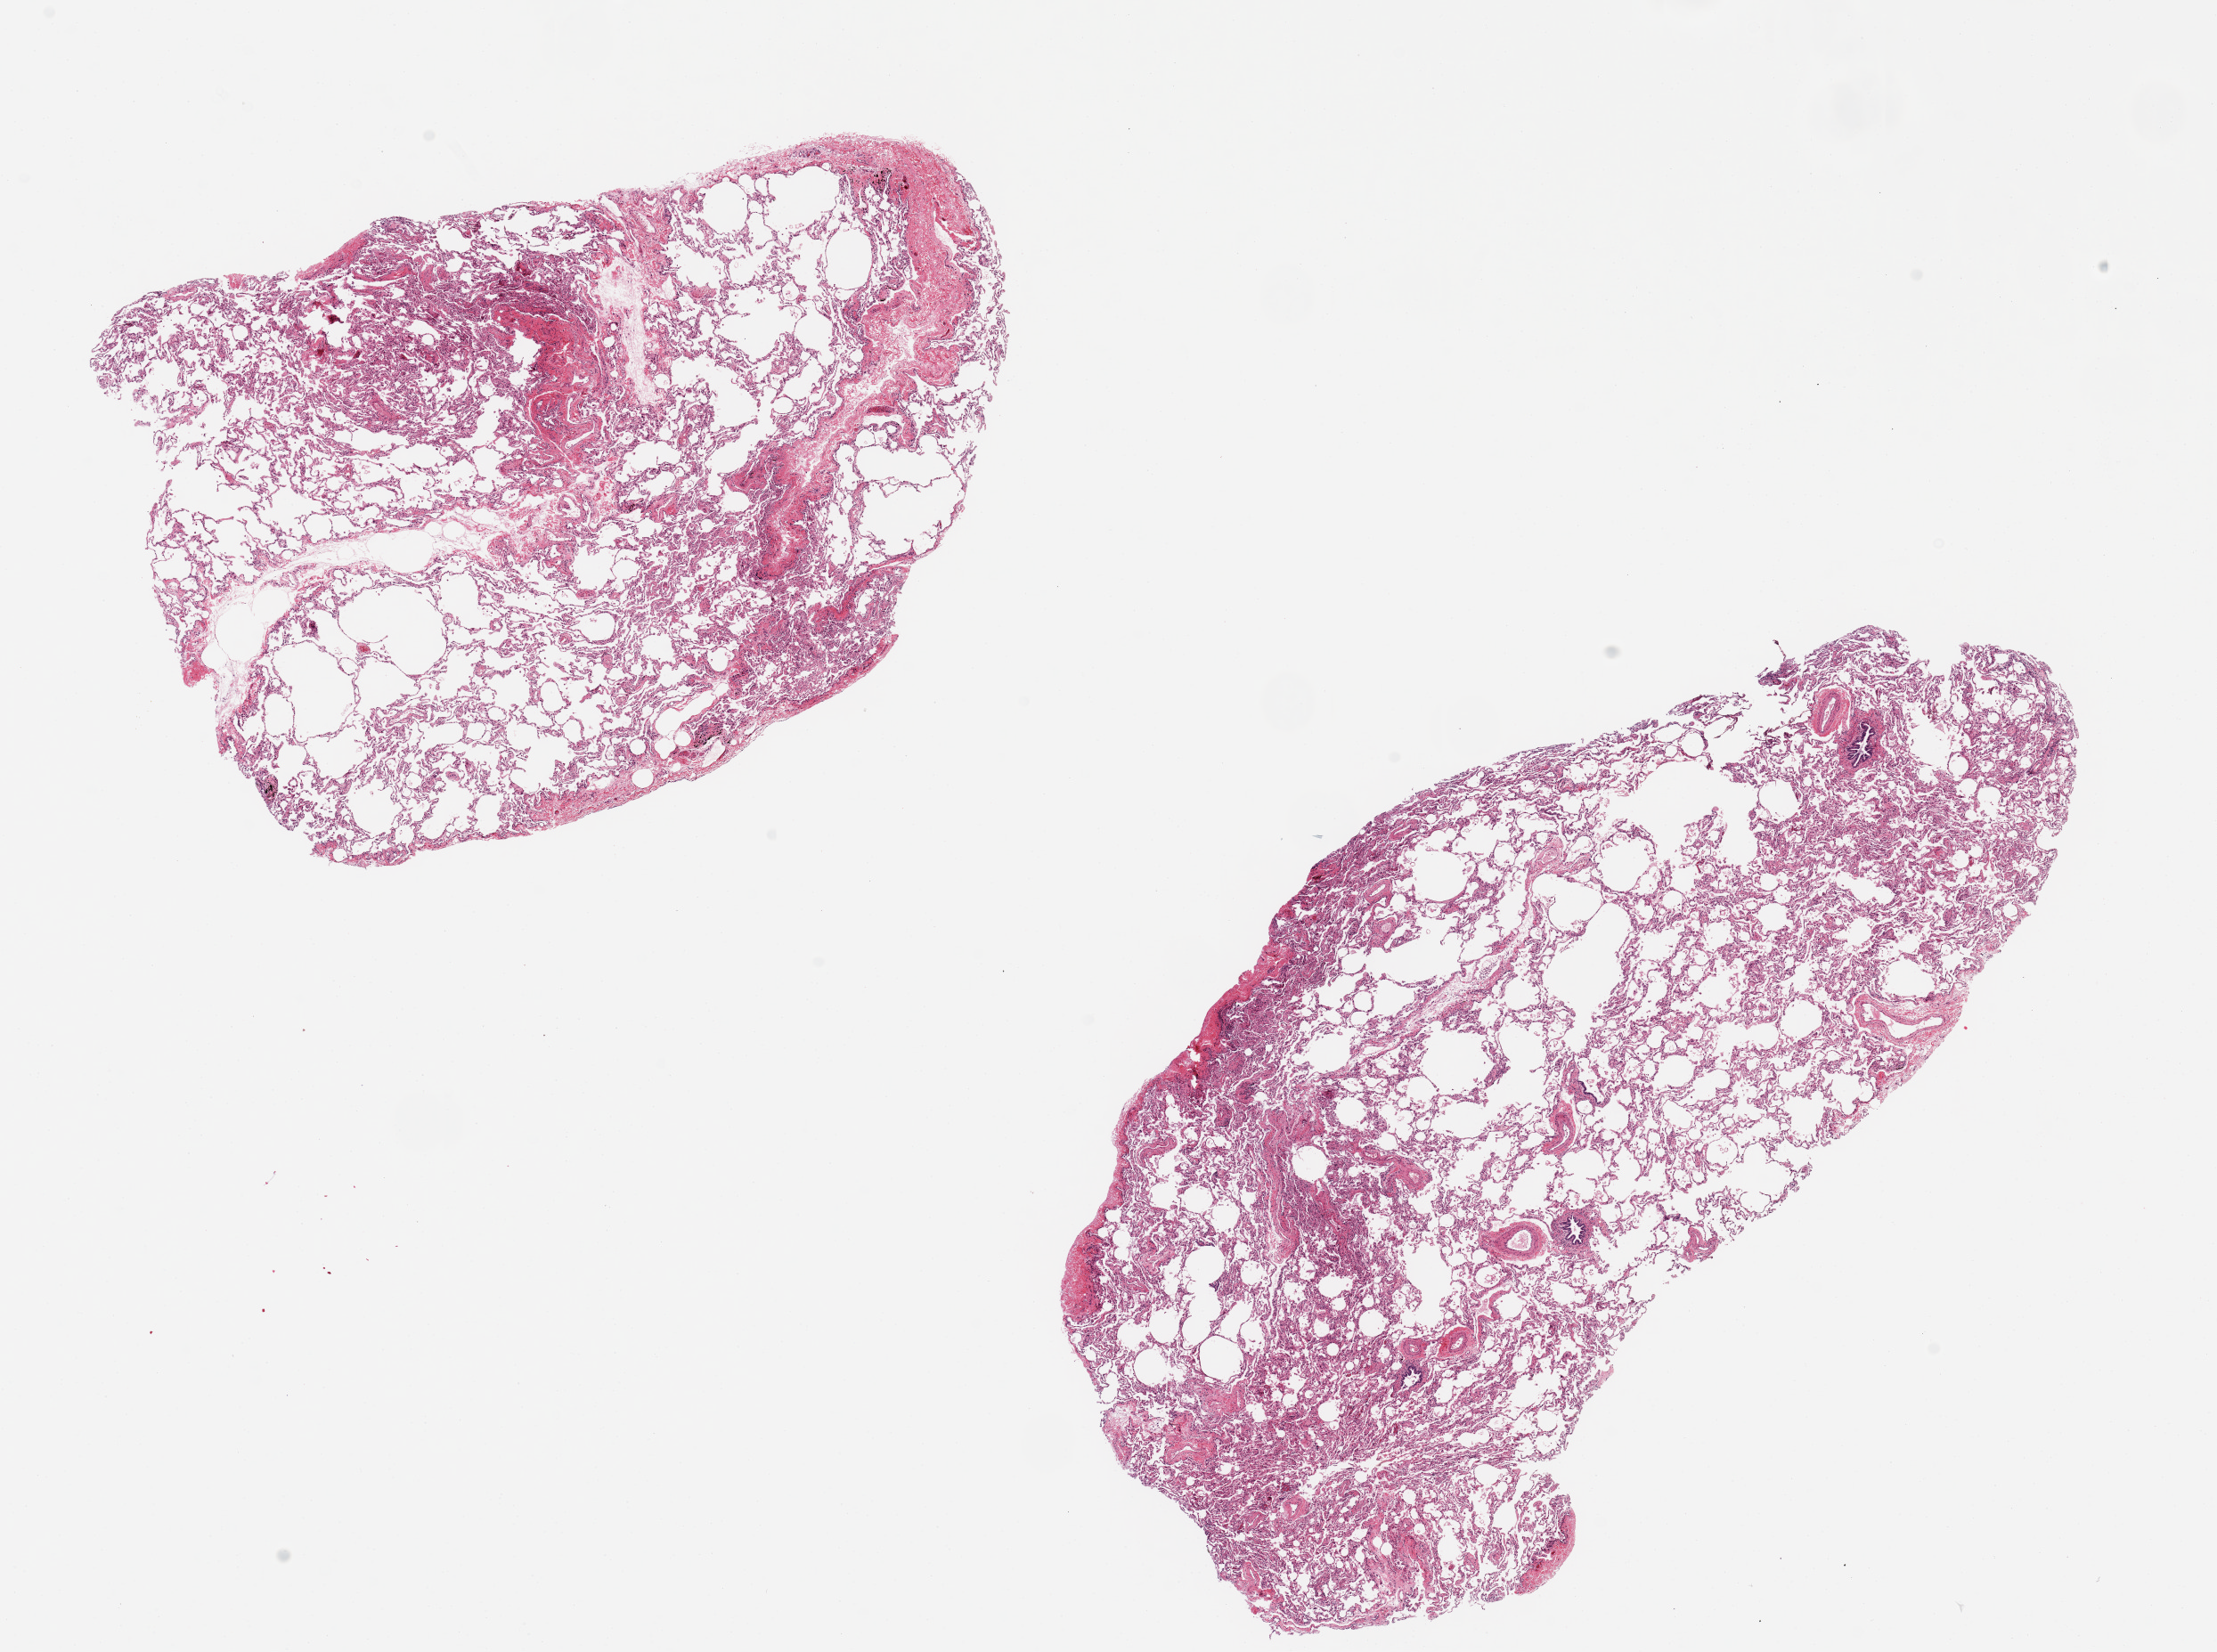
Hematoxylin and eosin (H&E) whole-slide image — whole scanned area (about 19.7 x 14.7 mm) shown as a low-resolution overview; PAXgene-fixed paraffin-embedded (PFPE) section; sampled site (target tissue): lung; donor tissue sample. Donor: male.
Review note (as recorded): 2 pieces ~9x6mm, diffuse emphysematous changes.